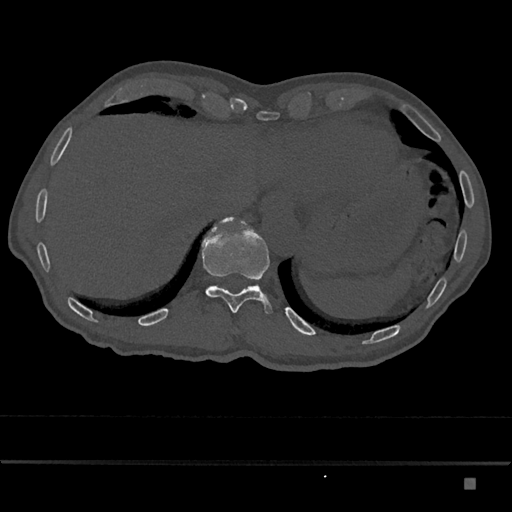
CT including the spine, one axial slice; position 675 of 797 along the scan axis; reconstruction kernel Br40s/3; bone window (W 1800 / L 400 HU); 512 × 512 image matrix. Patient: male, 72 years. From the clinical record (not read from this slice): primary cancer: prostate.
Structures marked on this image (semi-automatically segmented with operator editing):
- T11 vertebra: box from (x=201, y=216) to (x=273, y=314) px